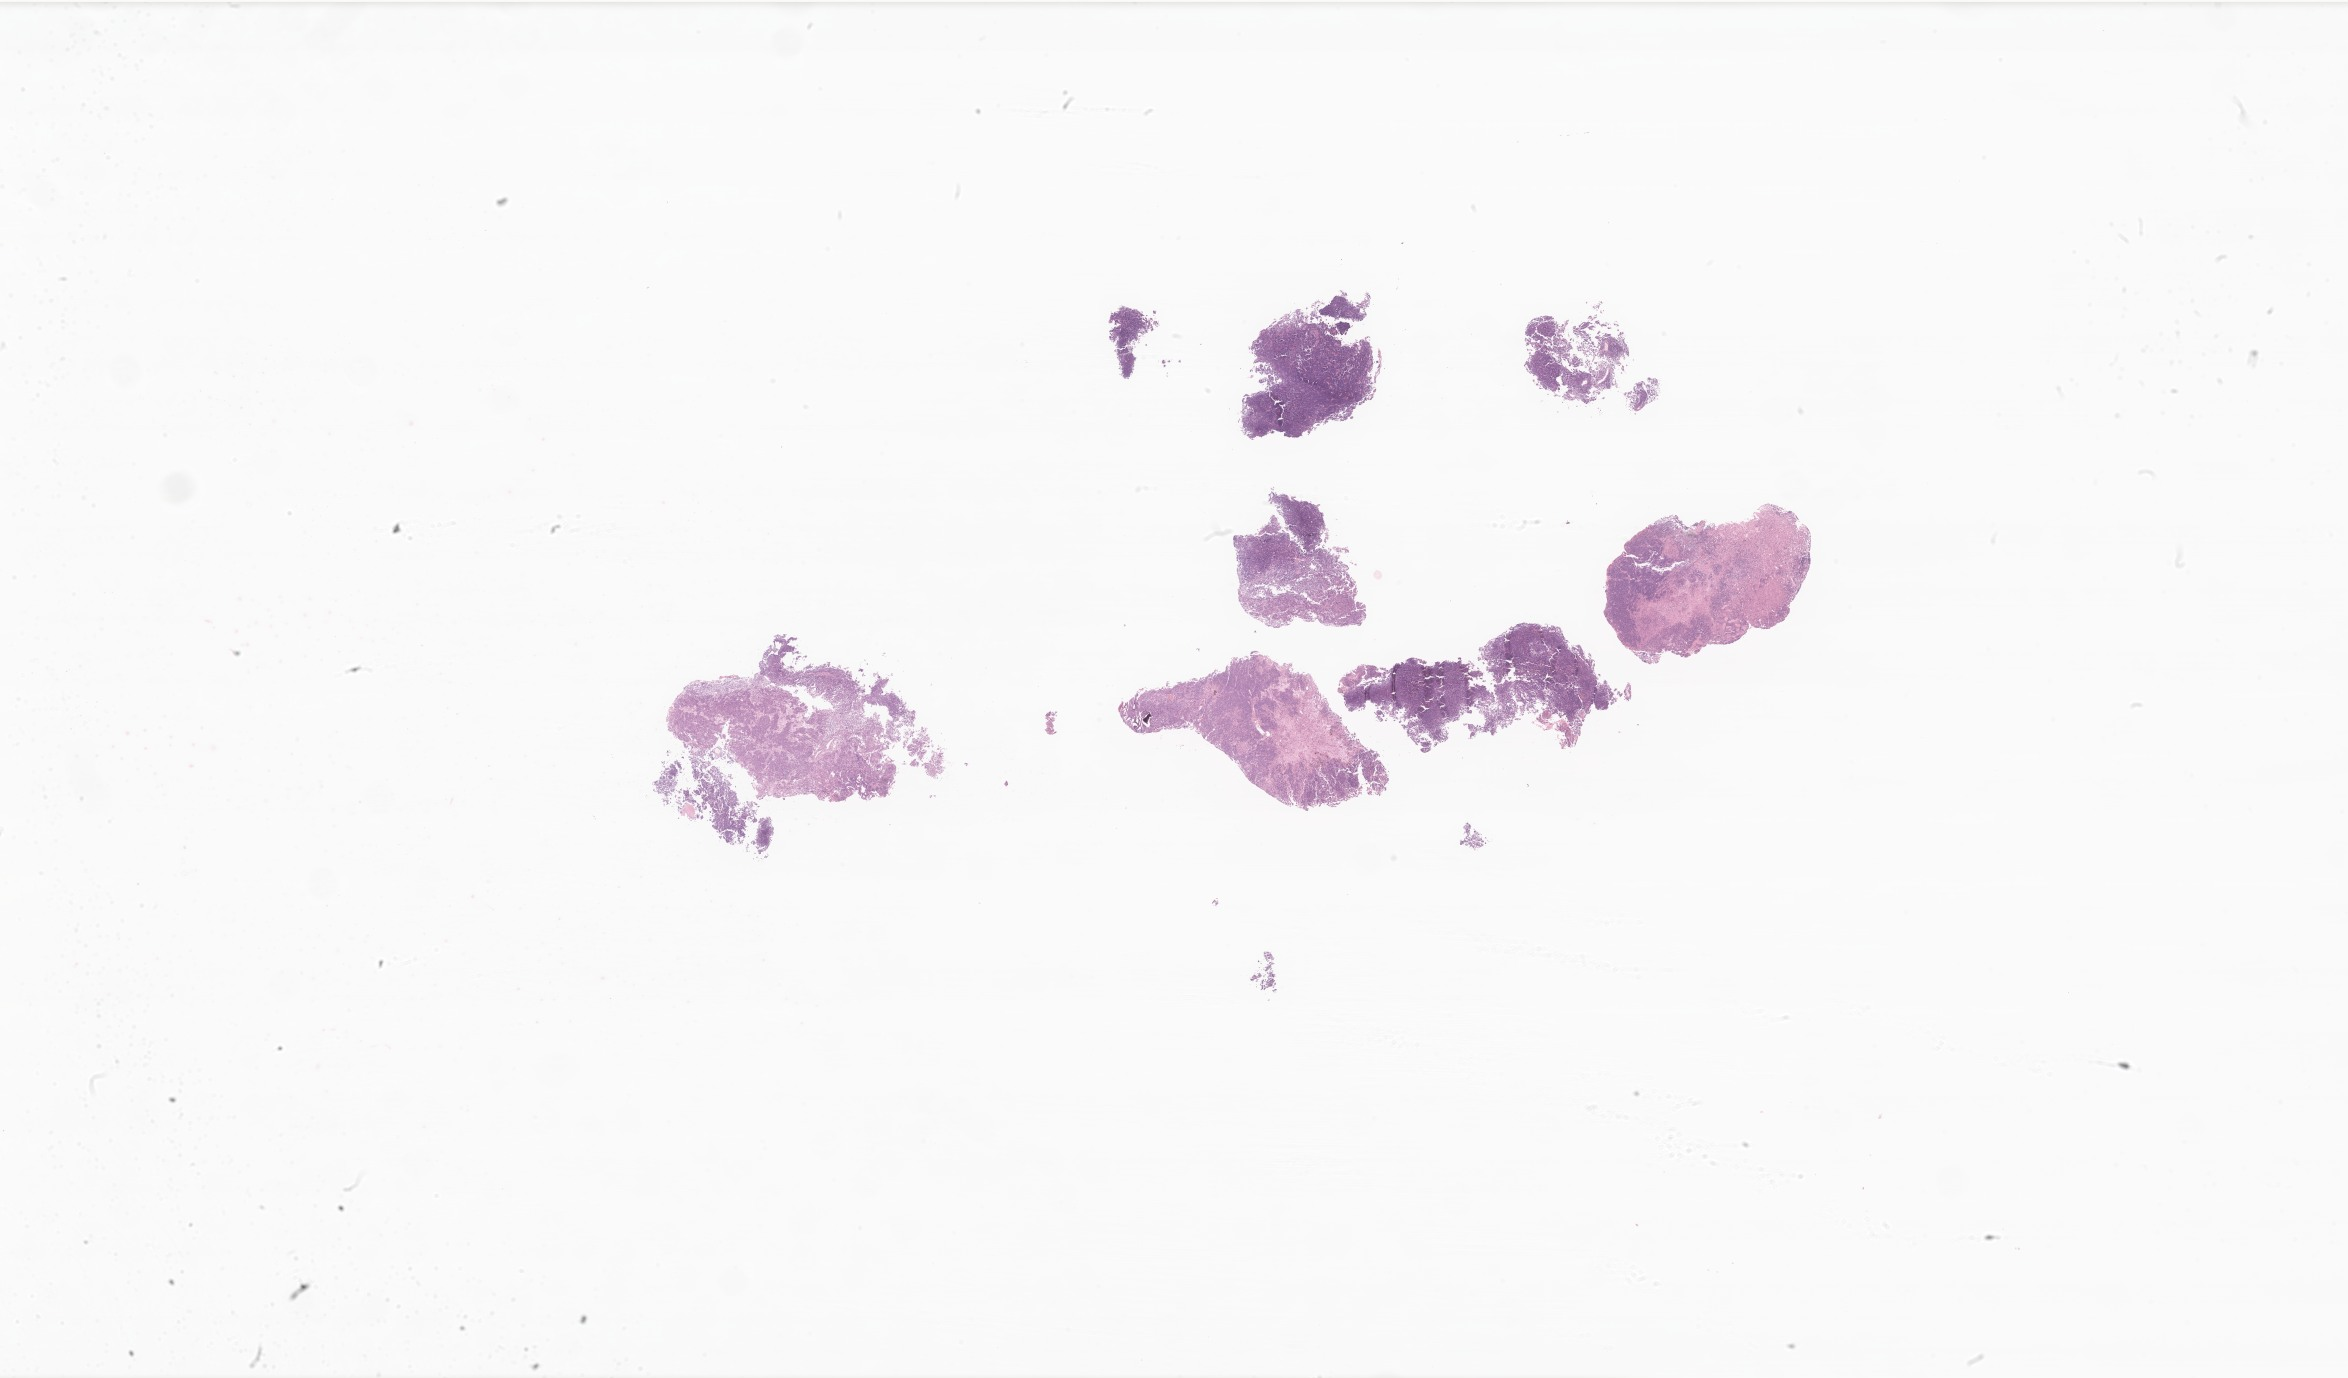
Digitized haematoxylin and eosin-stained section of tumor tissue from the cerebral ventricle — low-resolution overview of the scanned area, about 39.6 x 23.2 mm. Formalin-fixed paraffin-embedded section. Patient: female, age 118 months (9 years 10 months).
Diagnosis: Medulloblastoma, NOS.